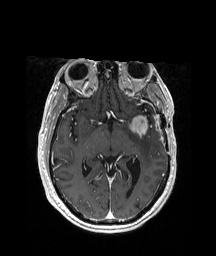
Brain MRI from a brain-tumour surgery series, one axial slice; slice 115 of 208 in the series (ordered by position); T1-weighted post-contrast; 1 mm slice thickness; 216 × 256 image matrix. Case-level facts recorded for this patient, not image findings: histopathology: Glioblastoma; WHO grade: 4.
Annotated regions visible in this slice (outlined manually by an expert reader):
- tumour: box from (x=134, y=114) to (x=153, y=134) px